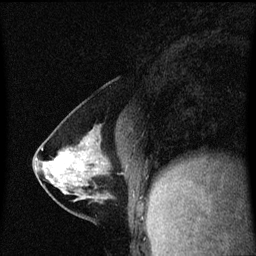
Breast MRI (dynamic contrast-enhanced), one sagittal slice. Dynamic contrast-enhanced series, image 2 of 3 at this slice position (ordered by acquisition). 1.5 T. TE 4.2 ms, TR 8.4 ms. 2 mm slice thickness. 256 × 256 image matrix, field of view 200 × 200 mm. Female patient, age 40 years. From the clinical record (not read from this slice): setting: breast cancer imaged before/during neoadjuvant chemotherapy; receptor status: triple-negative.
Outlined on this slice (semi-automatic segmentation, software-assisted and operator-edited):
- analysis volume of interest (the breast-tissue region the enhancement analysis was run in; not a lesion): bounding box (x1, y1, x2, y2) in pixels: (34, 142, 114, 199)
- tumour enhancement mask (voxels above the 70 % enhancement threshold inside the analysis volume of interest): (55, 158, 96, 171)